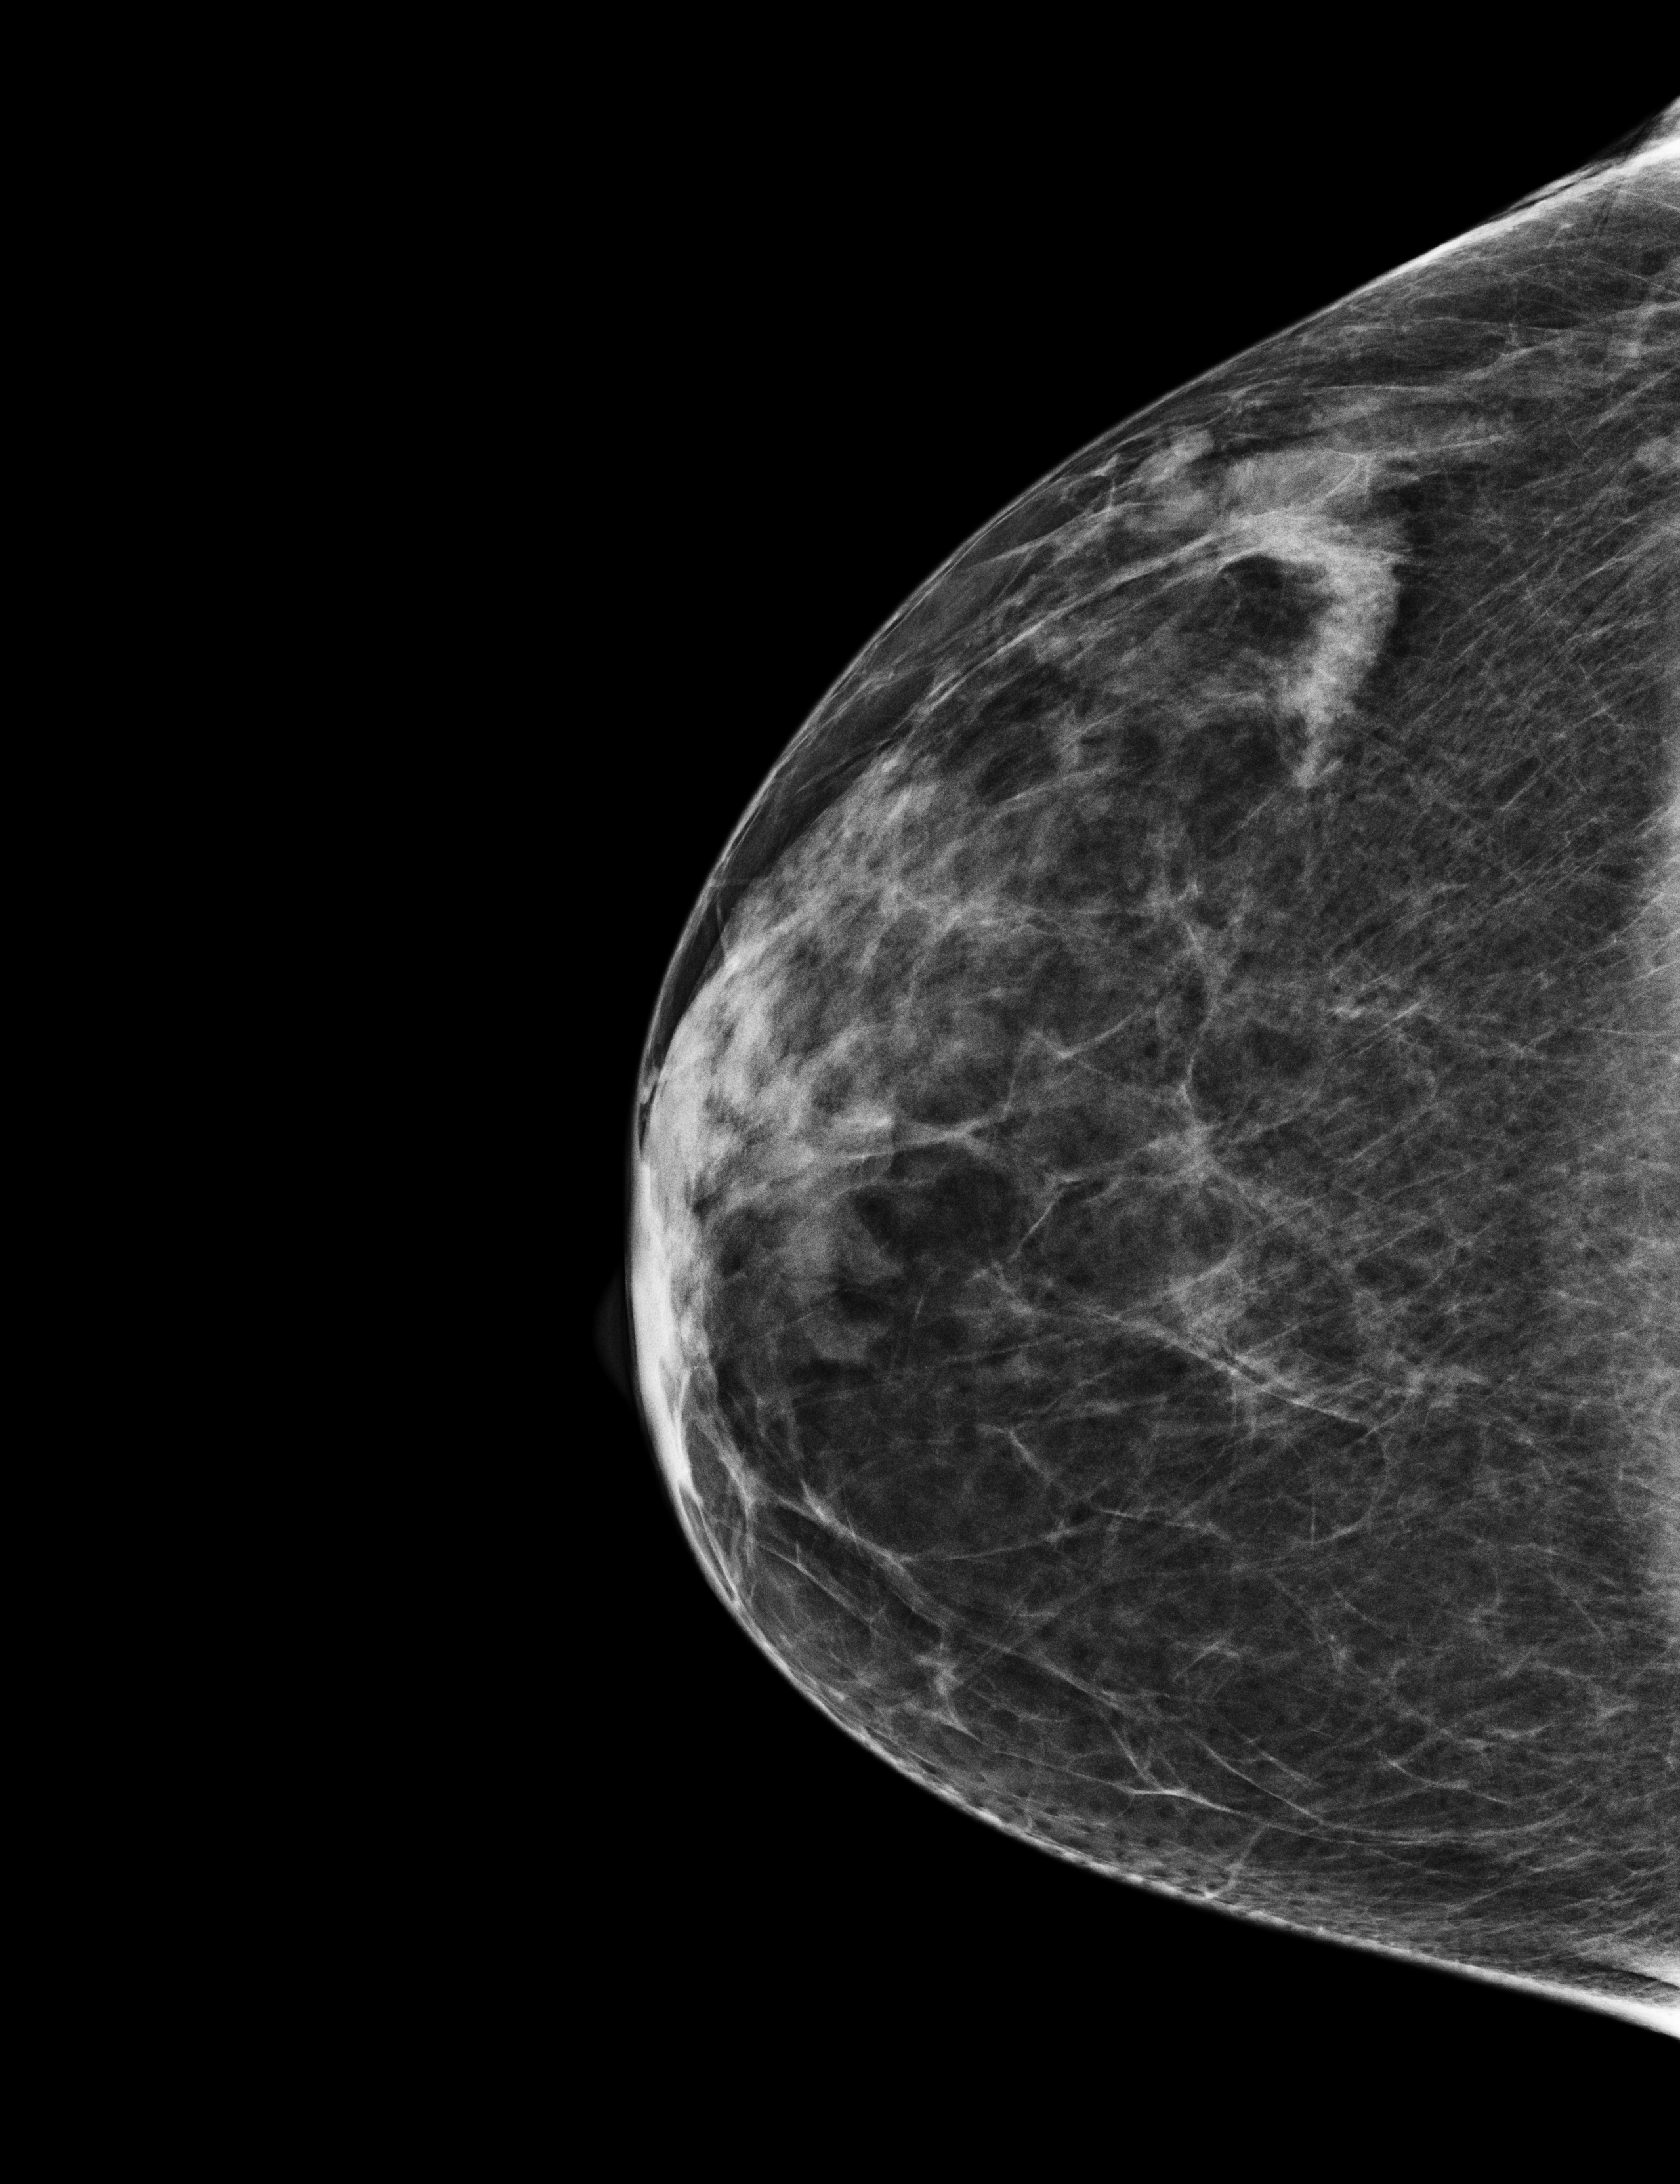
Diagnostic examination (additional views), compressed breast thickness 33 mm.
Image type: full-field digital mammogram. Breast: right. Projection: CC view.